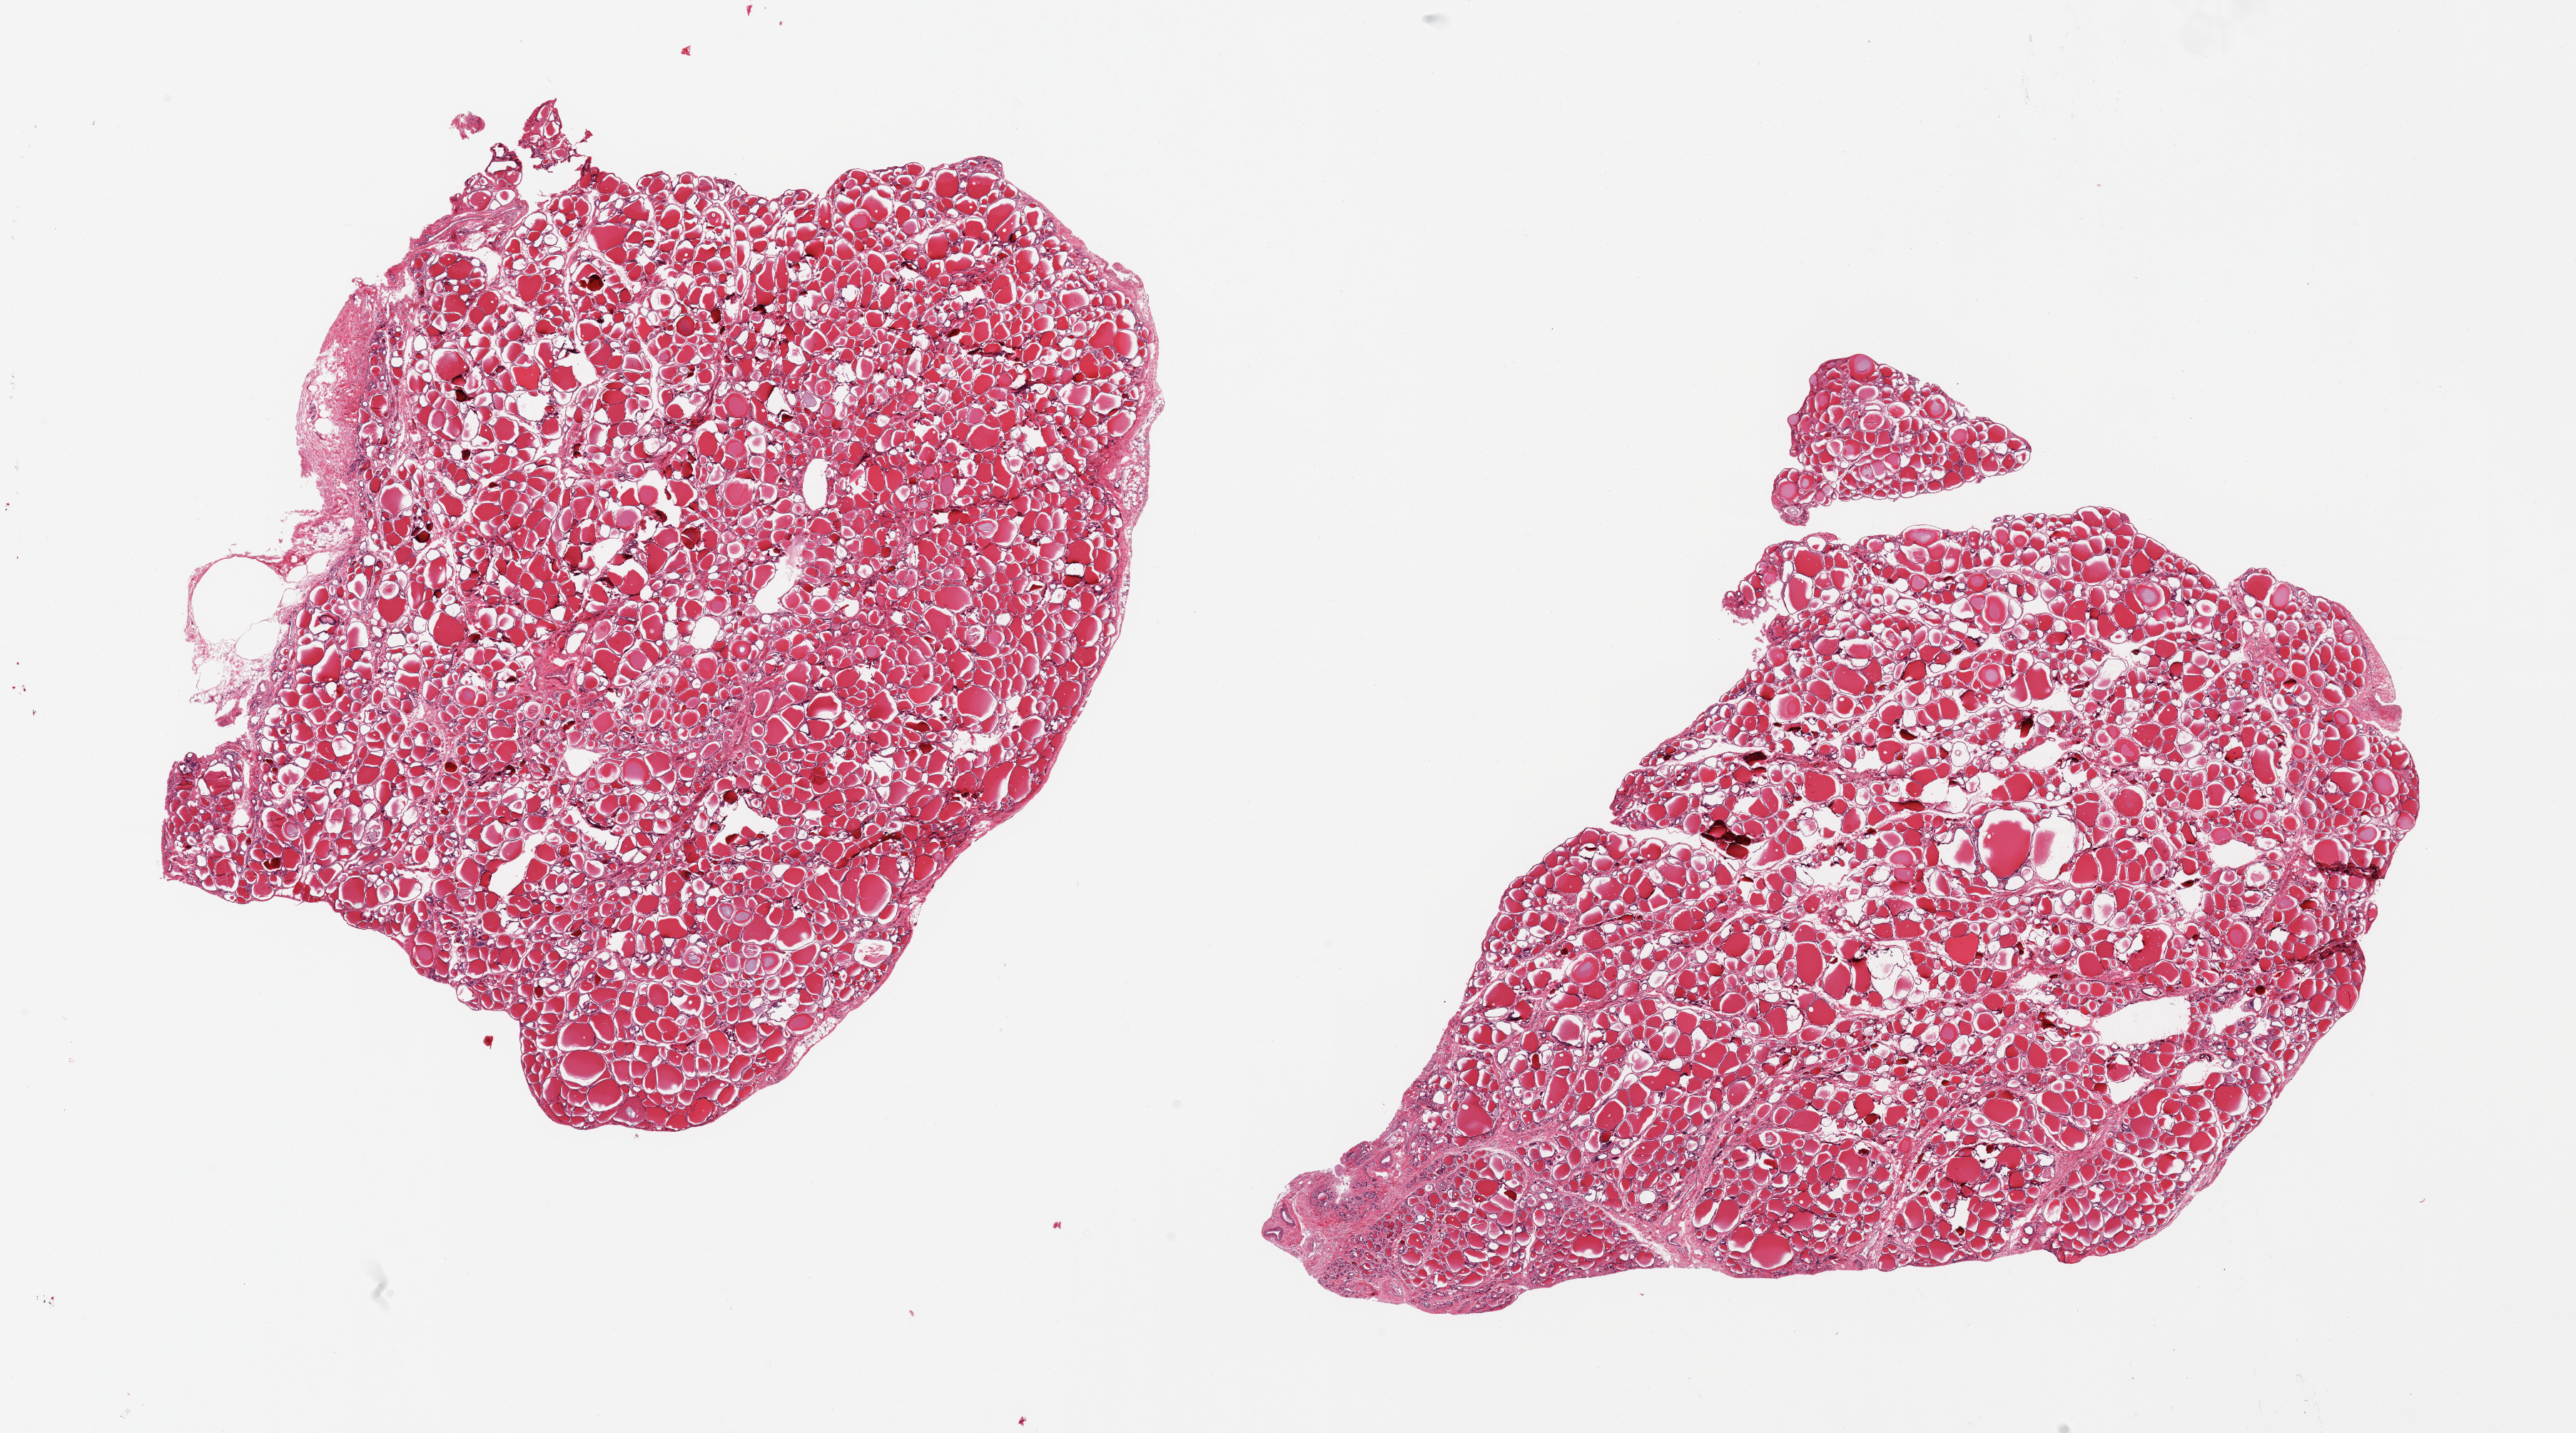
Haematoxylin and eosin whole-slide image, brightfield — low-resolution overview of the scanned area, about 28.5 x 15.9 mm. PAXgene-fixed, paraffin-embedded tissue. Target tissue: thyroid. Tissue donor sample. Male donor.
Reviewer comment on this tissue sample: 2 pieces.